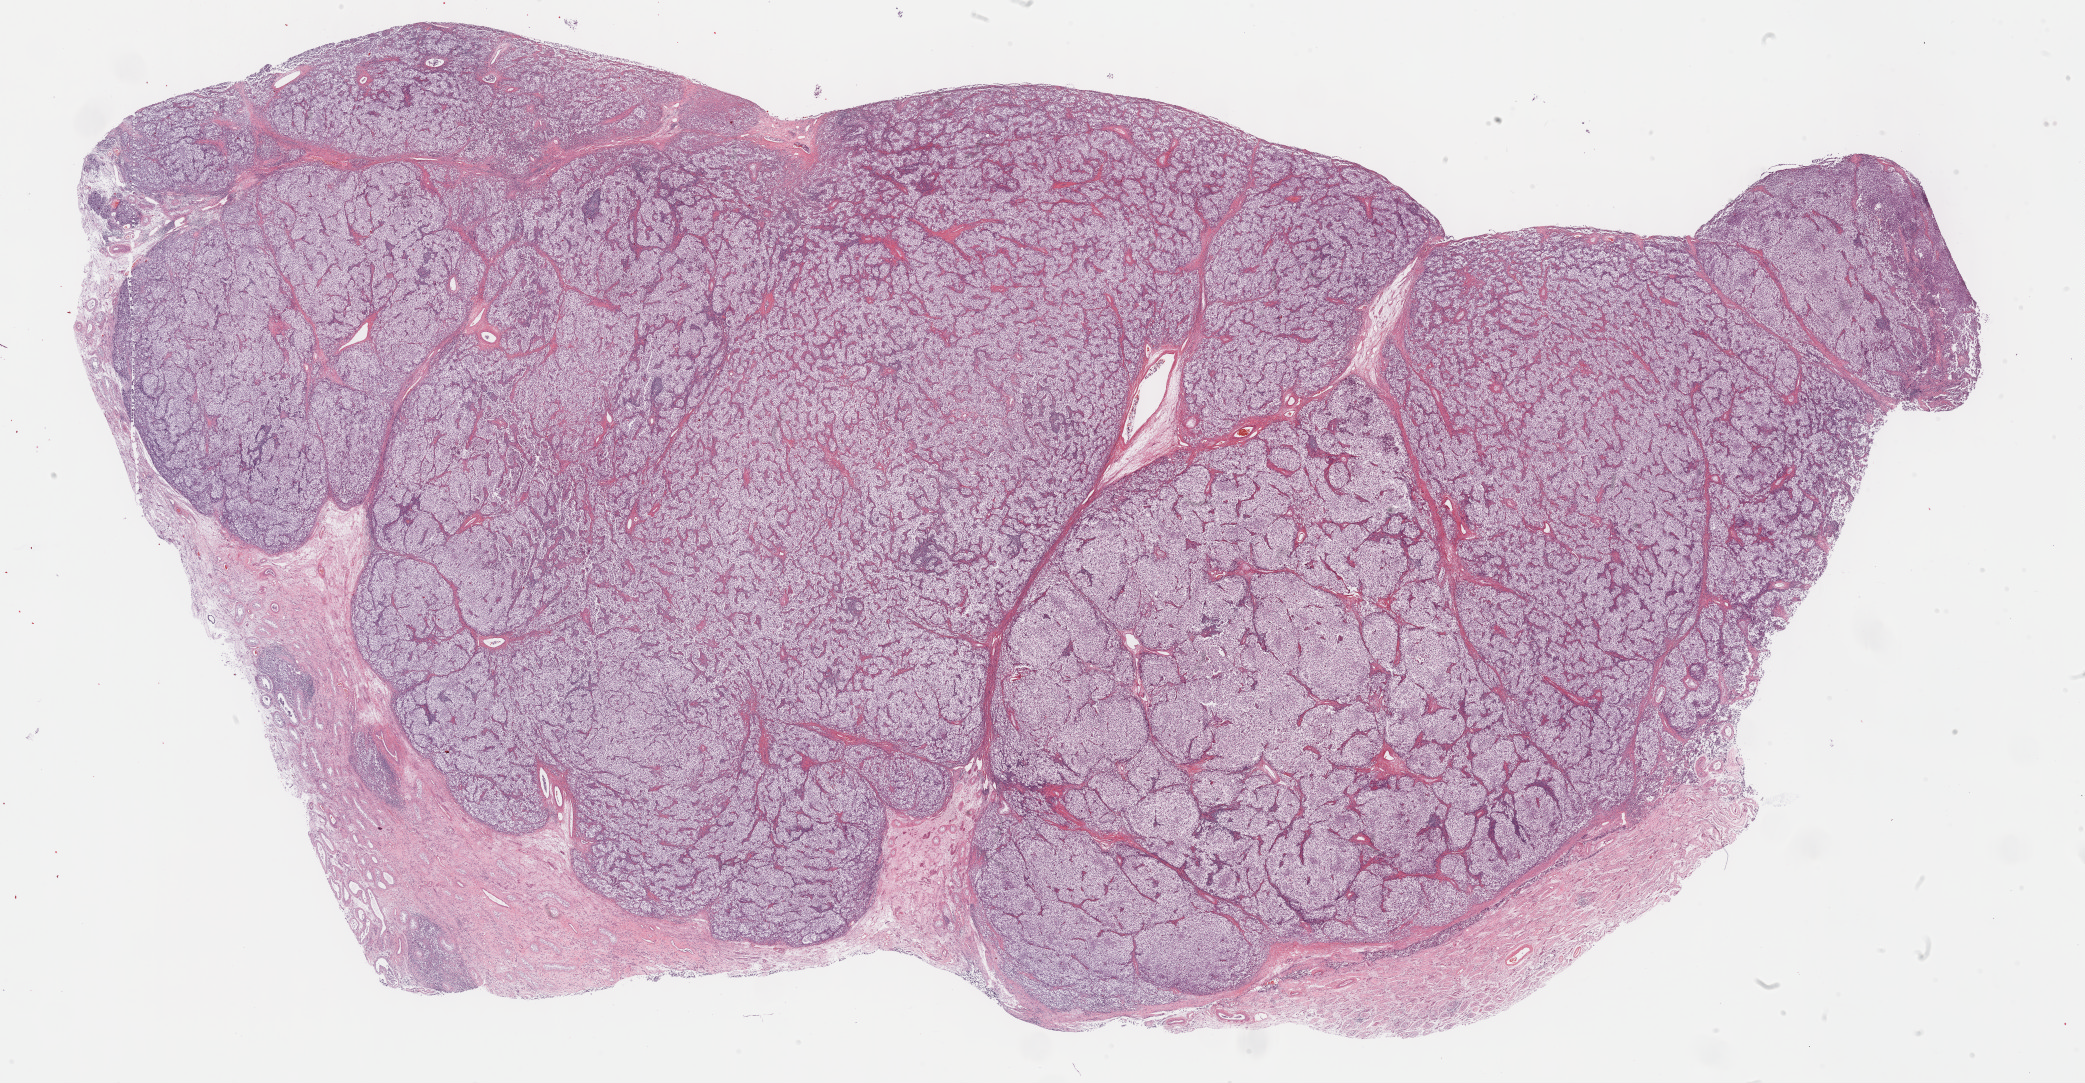
Hematoxylin and eosin (H&E) stained whole-slide image — whole scanned area (about 33.7 x 17.5 mm) shown as a low-resolution overview; formalin-fixed paraffin-embedded (FFPE) diagnostic section; testis, primary tumour sample. Patient: male, age at initial diagnosis 52 years.
- AJCC pathologic stage: IB (6th edition)
- diagnosis: Seminoma, NOS
- TNM: T2 NX M0